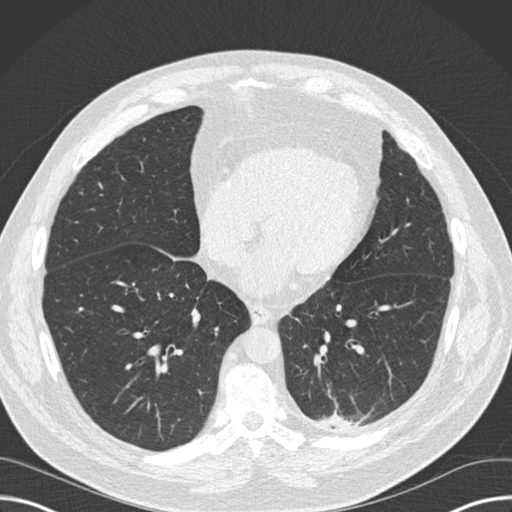
Low-dose screening chest CT, one axial slice; slice 59 of 160 in the series (ordered by position); reconstruction kernel B30f; lung window (W 1500 / L -600 HU); 512 × 512 image matrix.
Structures marked on this image (outlined manually by an expert reader):
- lesion 1 (tumor, upper lobe of left lung): bounding box [x1, y1, x2, y2] px = [322, 414, 355, 427]